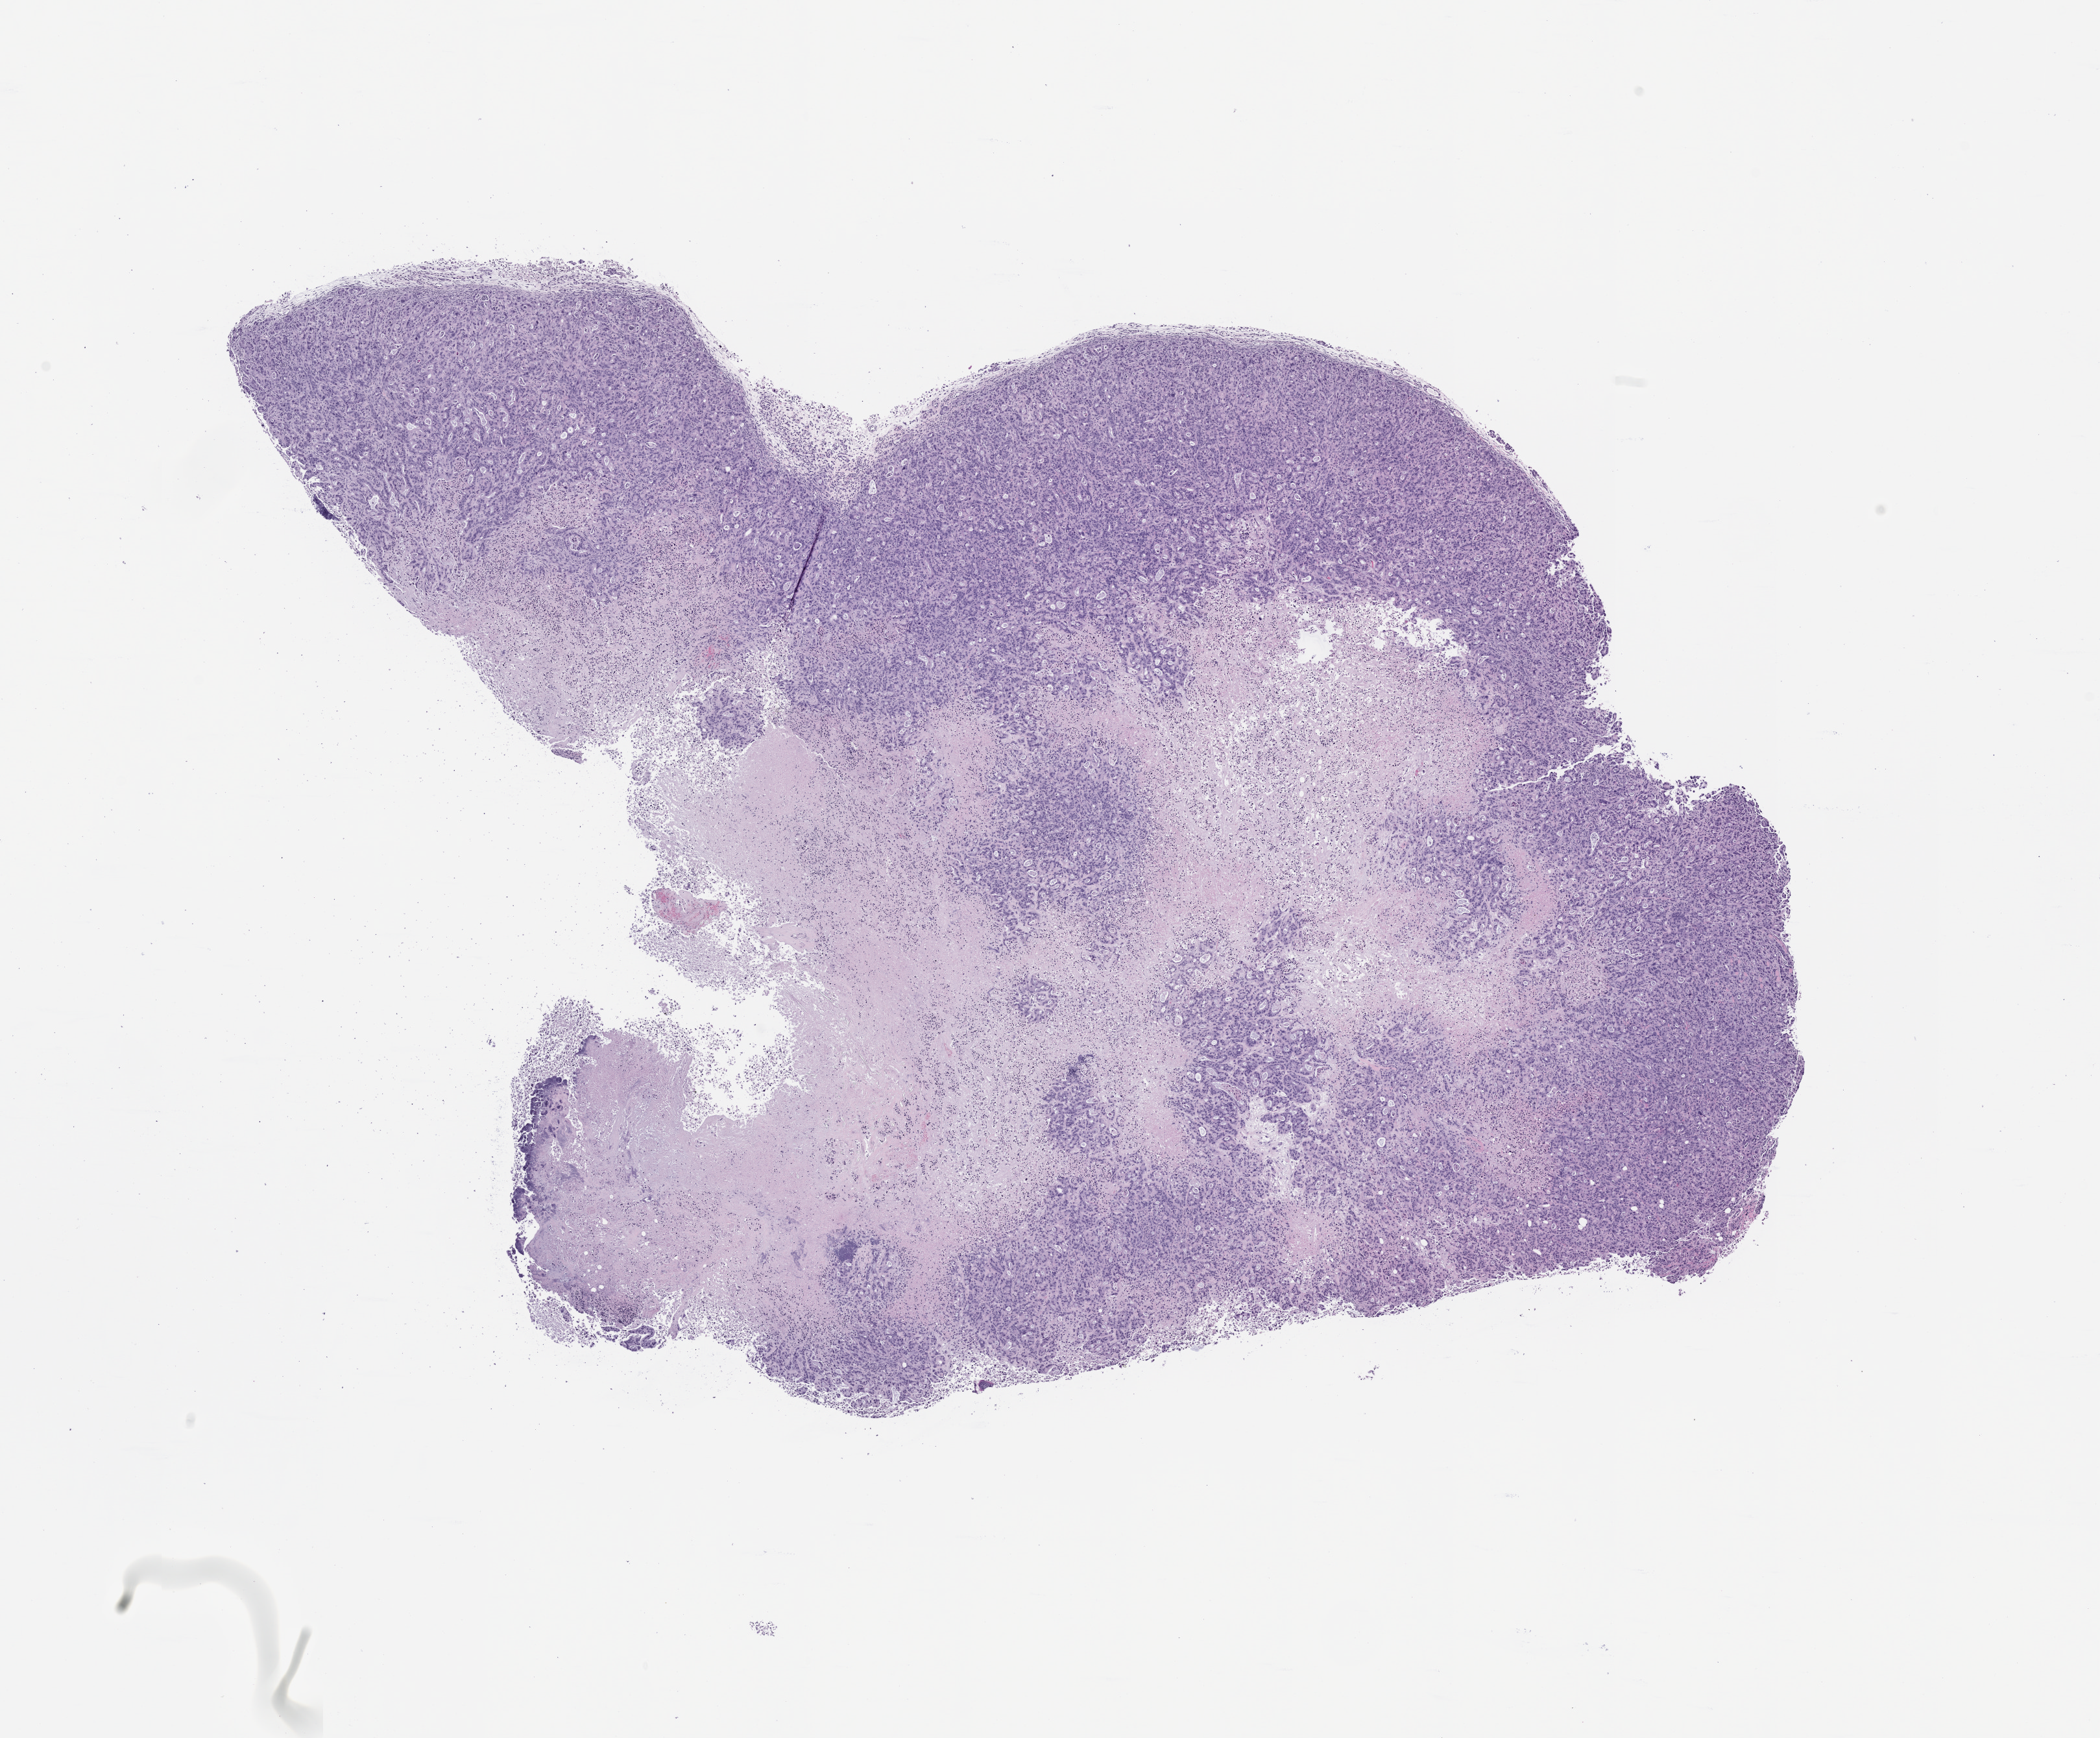
Whole-slide image, H&E: patient-derived xenograft (human tumor grown in a mouse), shown as a low-resolution overview of the whole scanned area (about 13.0 x 10.8 mm); formalin-fixed, paraffin-embedded (FFPE) tissue; tumor site category: pancreas.
Originating patient diagnosis: Pancreatic Adenocarcinoma.